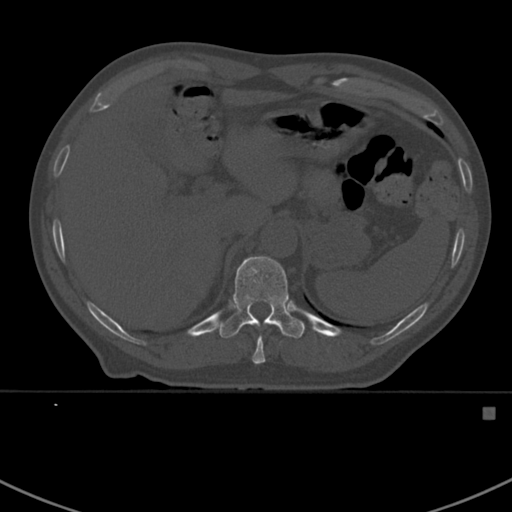
CT including the spine, one axial slice. Position 353 of 412 along the scan axis. Bone window (W 1800 / L 400 HU). 1.5 mm slice thickness. 512 × 512 image matrix, field of view 358 × 358 mm. Male patient, age 59 years. Case-level facts recorded for this patient, not image findings: primary cancer: prostate.
Structures marked on this image (semi-automatically segmented with operator editing):
- T10 vertebra: bounding box (x1, y1, x2, y2) in pixels: (252, 337, 265, 364)
- T11 vertebra: (216, 256, 305, 338)